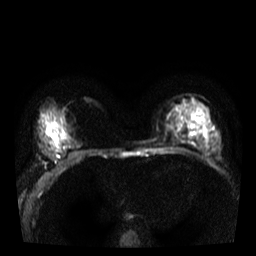
Breast MRI, one axial slice. Slice 18 of 40 in the series (ordered by position). Diffusion-weighted series; image 2 of 4 stored at this slice position (different b-values; order by instance number). 3 T. 5 mm slice thickness. 256 × 256 image matrix, field of view 320 × 320 mm. Female patient.
Annotated regions visible in this slice (manually delineated by an expert):
- tumour on diffusion-weighted imaging: bounding box (x1, y1, x2, y2) in pixels: (191, 113, 201, 122)